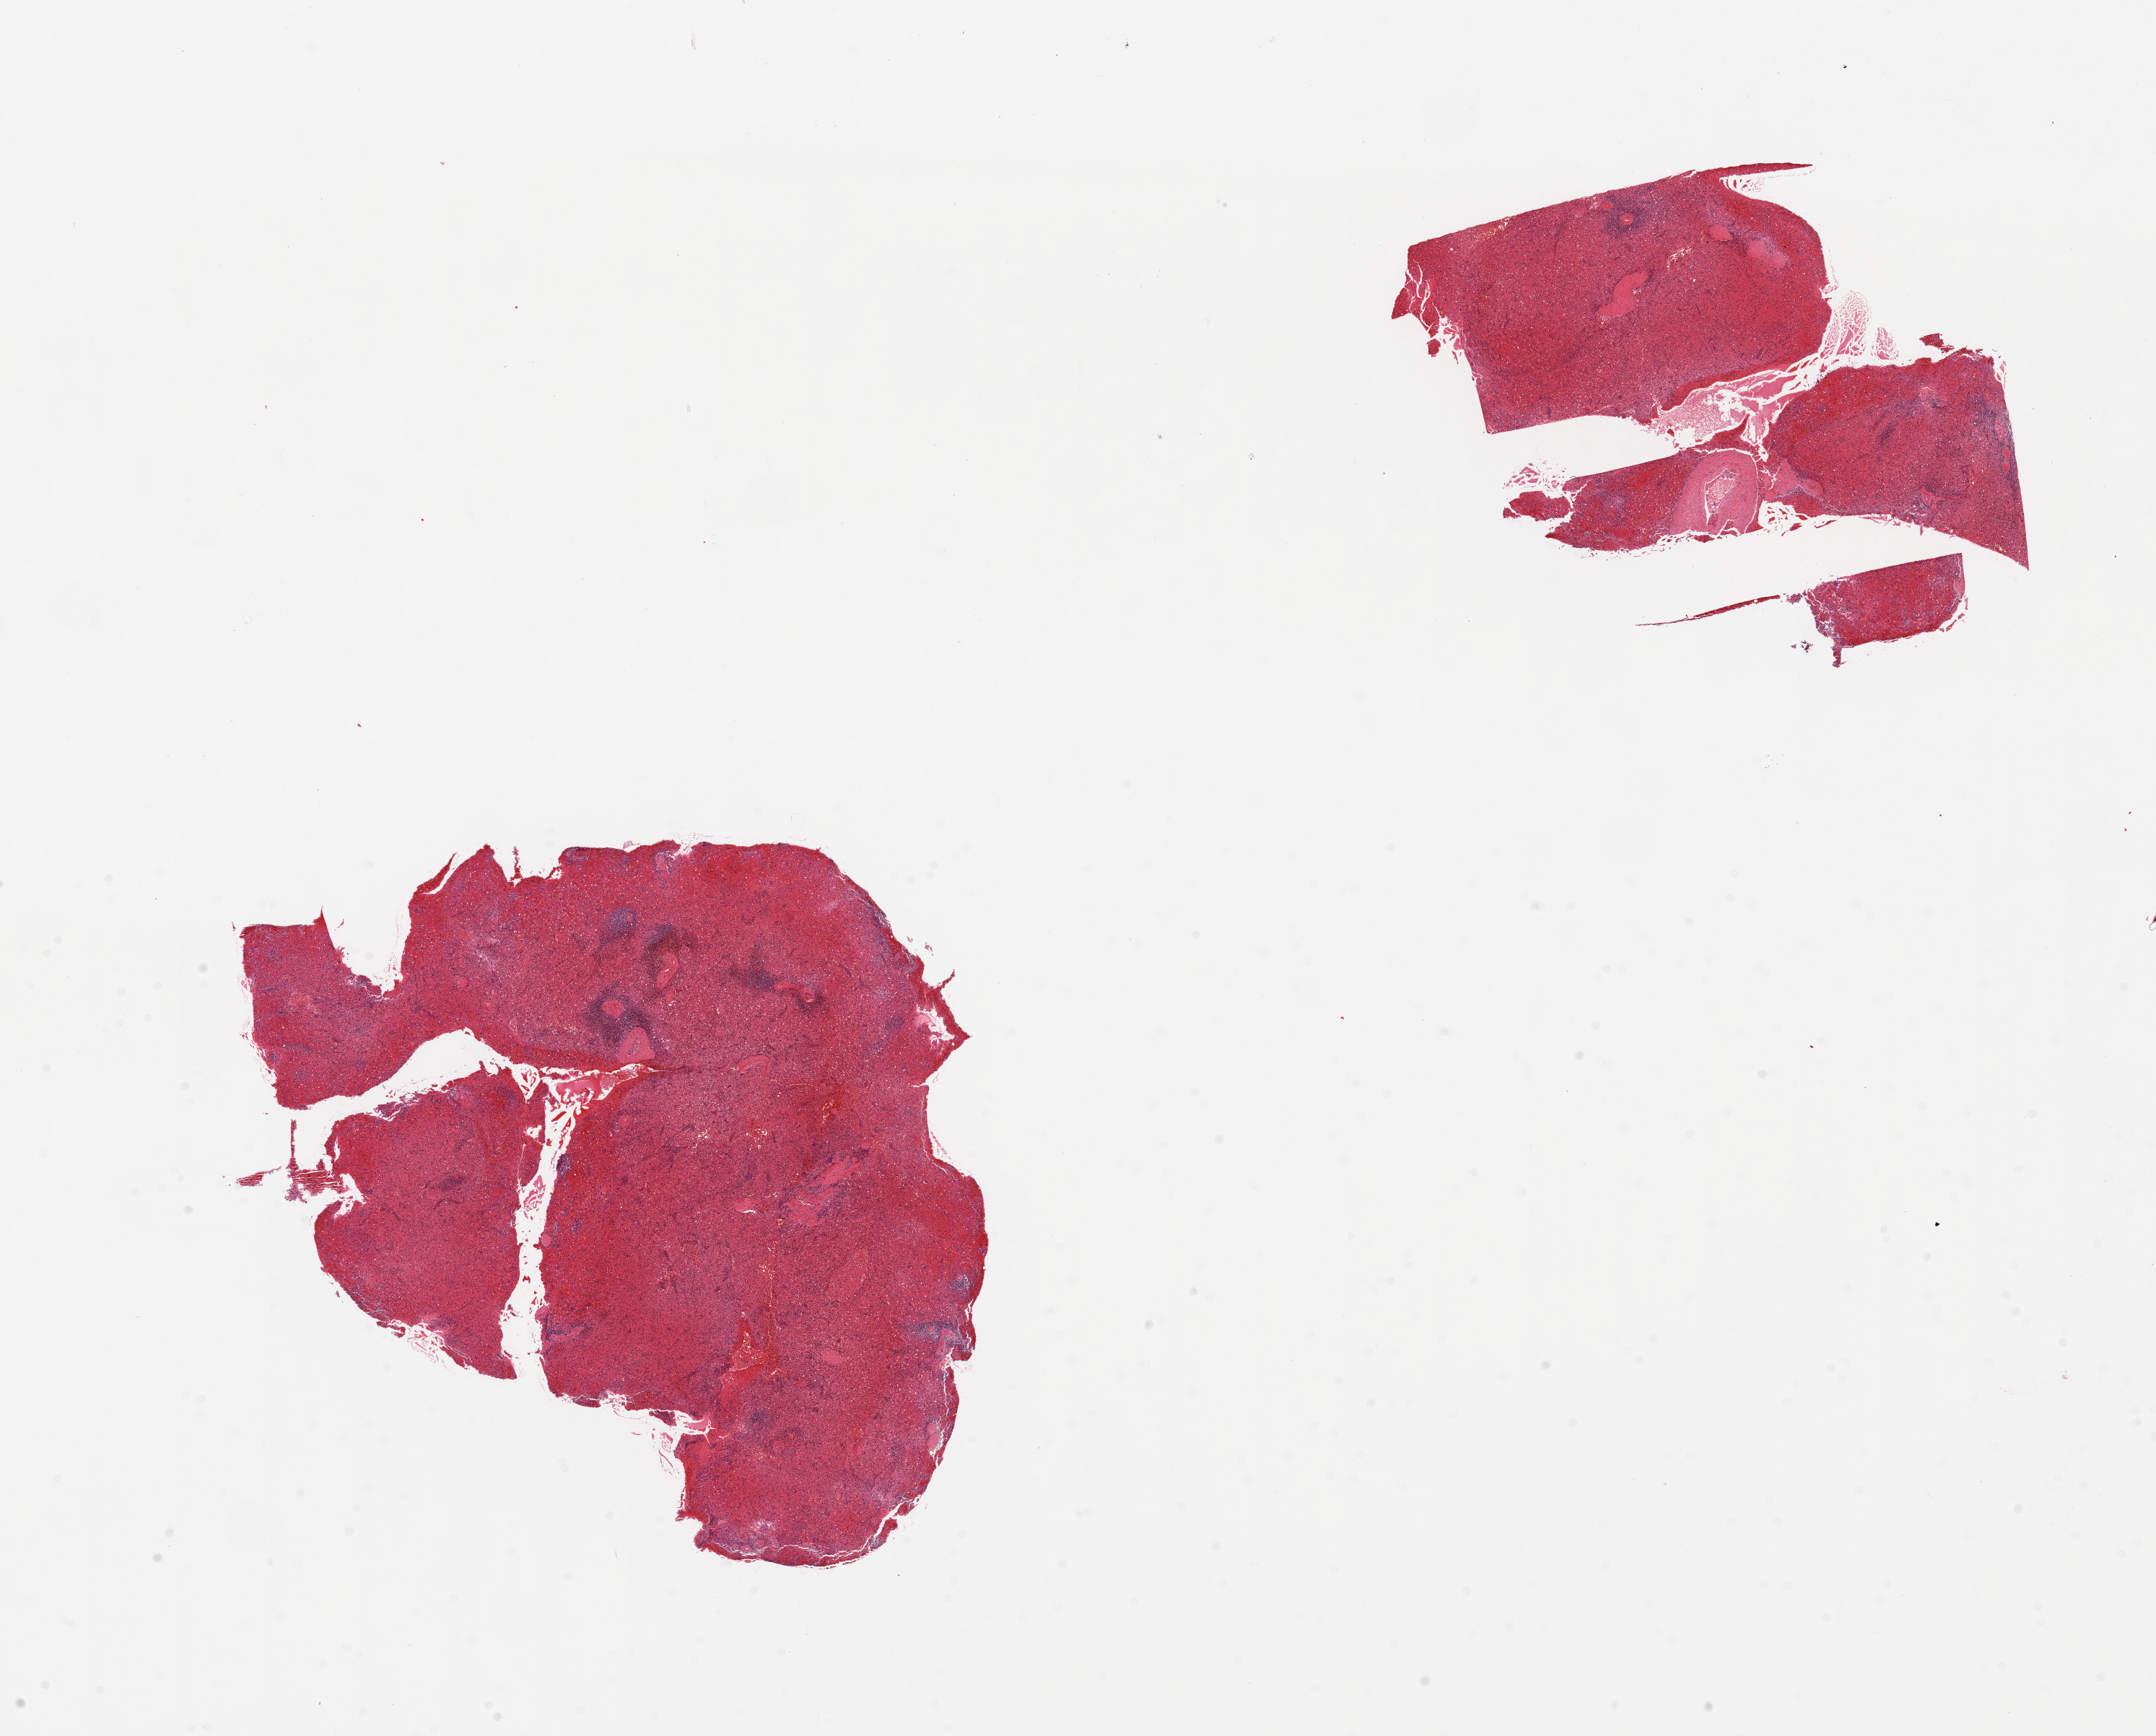
Whole-slide image, H&E stain, brightfield — shown as a low-resolution overview of the whole scanned area (about 23.6 x 19.0 mm, acquisition: 20x scan), PAXgene-fixed paraffin-embedded (PFPE) section, section of spleen (target tissue), donor tissue sample. Donor sex: male.
Reviewer comment on this tissue sample: 2 pieces; severe congestion.